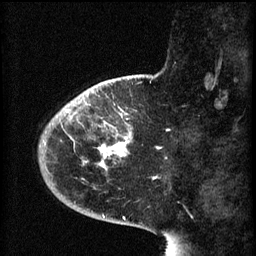
Breast MRI (dynamic contrast-enhanced), one sagittal slice; position 15 of 60 along the scan axis; 3 images stored at this slice position (order not interpretable as contrast timing); 1.5 T; TE 4.2 ms, TR 8.1 ms; 2 mm slice thickness; 256 × 256 image matrix, field of view 200 × 200 mm. Patient: female, 44 years.
Structures marked on this image (semi-automatically segmented with operator editing):
- analysis volume of interest (the breast-tissue region the enhancement analysis was run in; not a lesion): bounding box [x1, y1, x2, y2] px = [59, 110, 133, 169]
- tumour enhancement mask (voxels above the 70 % enhancement threshold inside the analysis volume of interest): [59, 110, 131, 169]